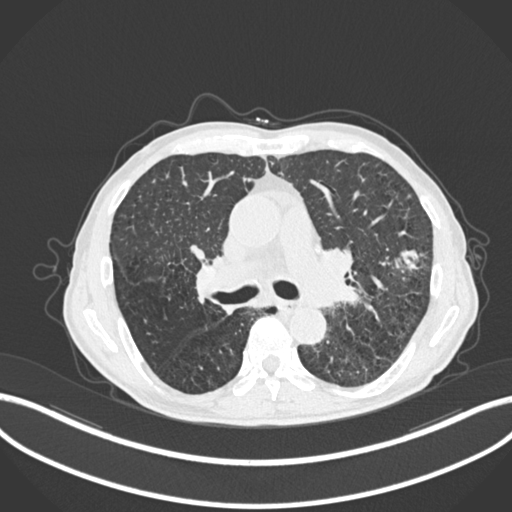
Chest CT, one axial slice; position 151 of 287 along the scan axis; lung window (W 1500 / L -600 HU); 1 mm slice thickness; 512 × 512 image matrix, field of view 400 × 400 mm. Male patient, age 74 years. Case-level facts recorded for this patient, not image findings: clinical TNM (as recorded): T2a N1 M0.
Structures marked on this image (rectangle marked by the reading radiologist):
- lung tumour (recorded histology: adenocarcinoma): bounding box [x1, y1, x2, y2] px = [394, 246, 423, 277]